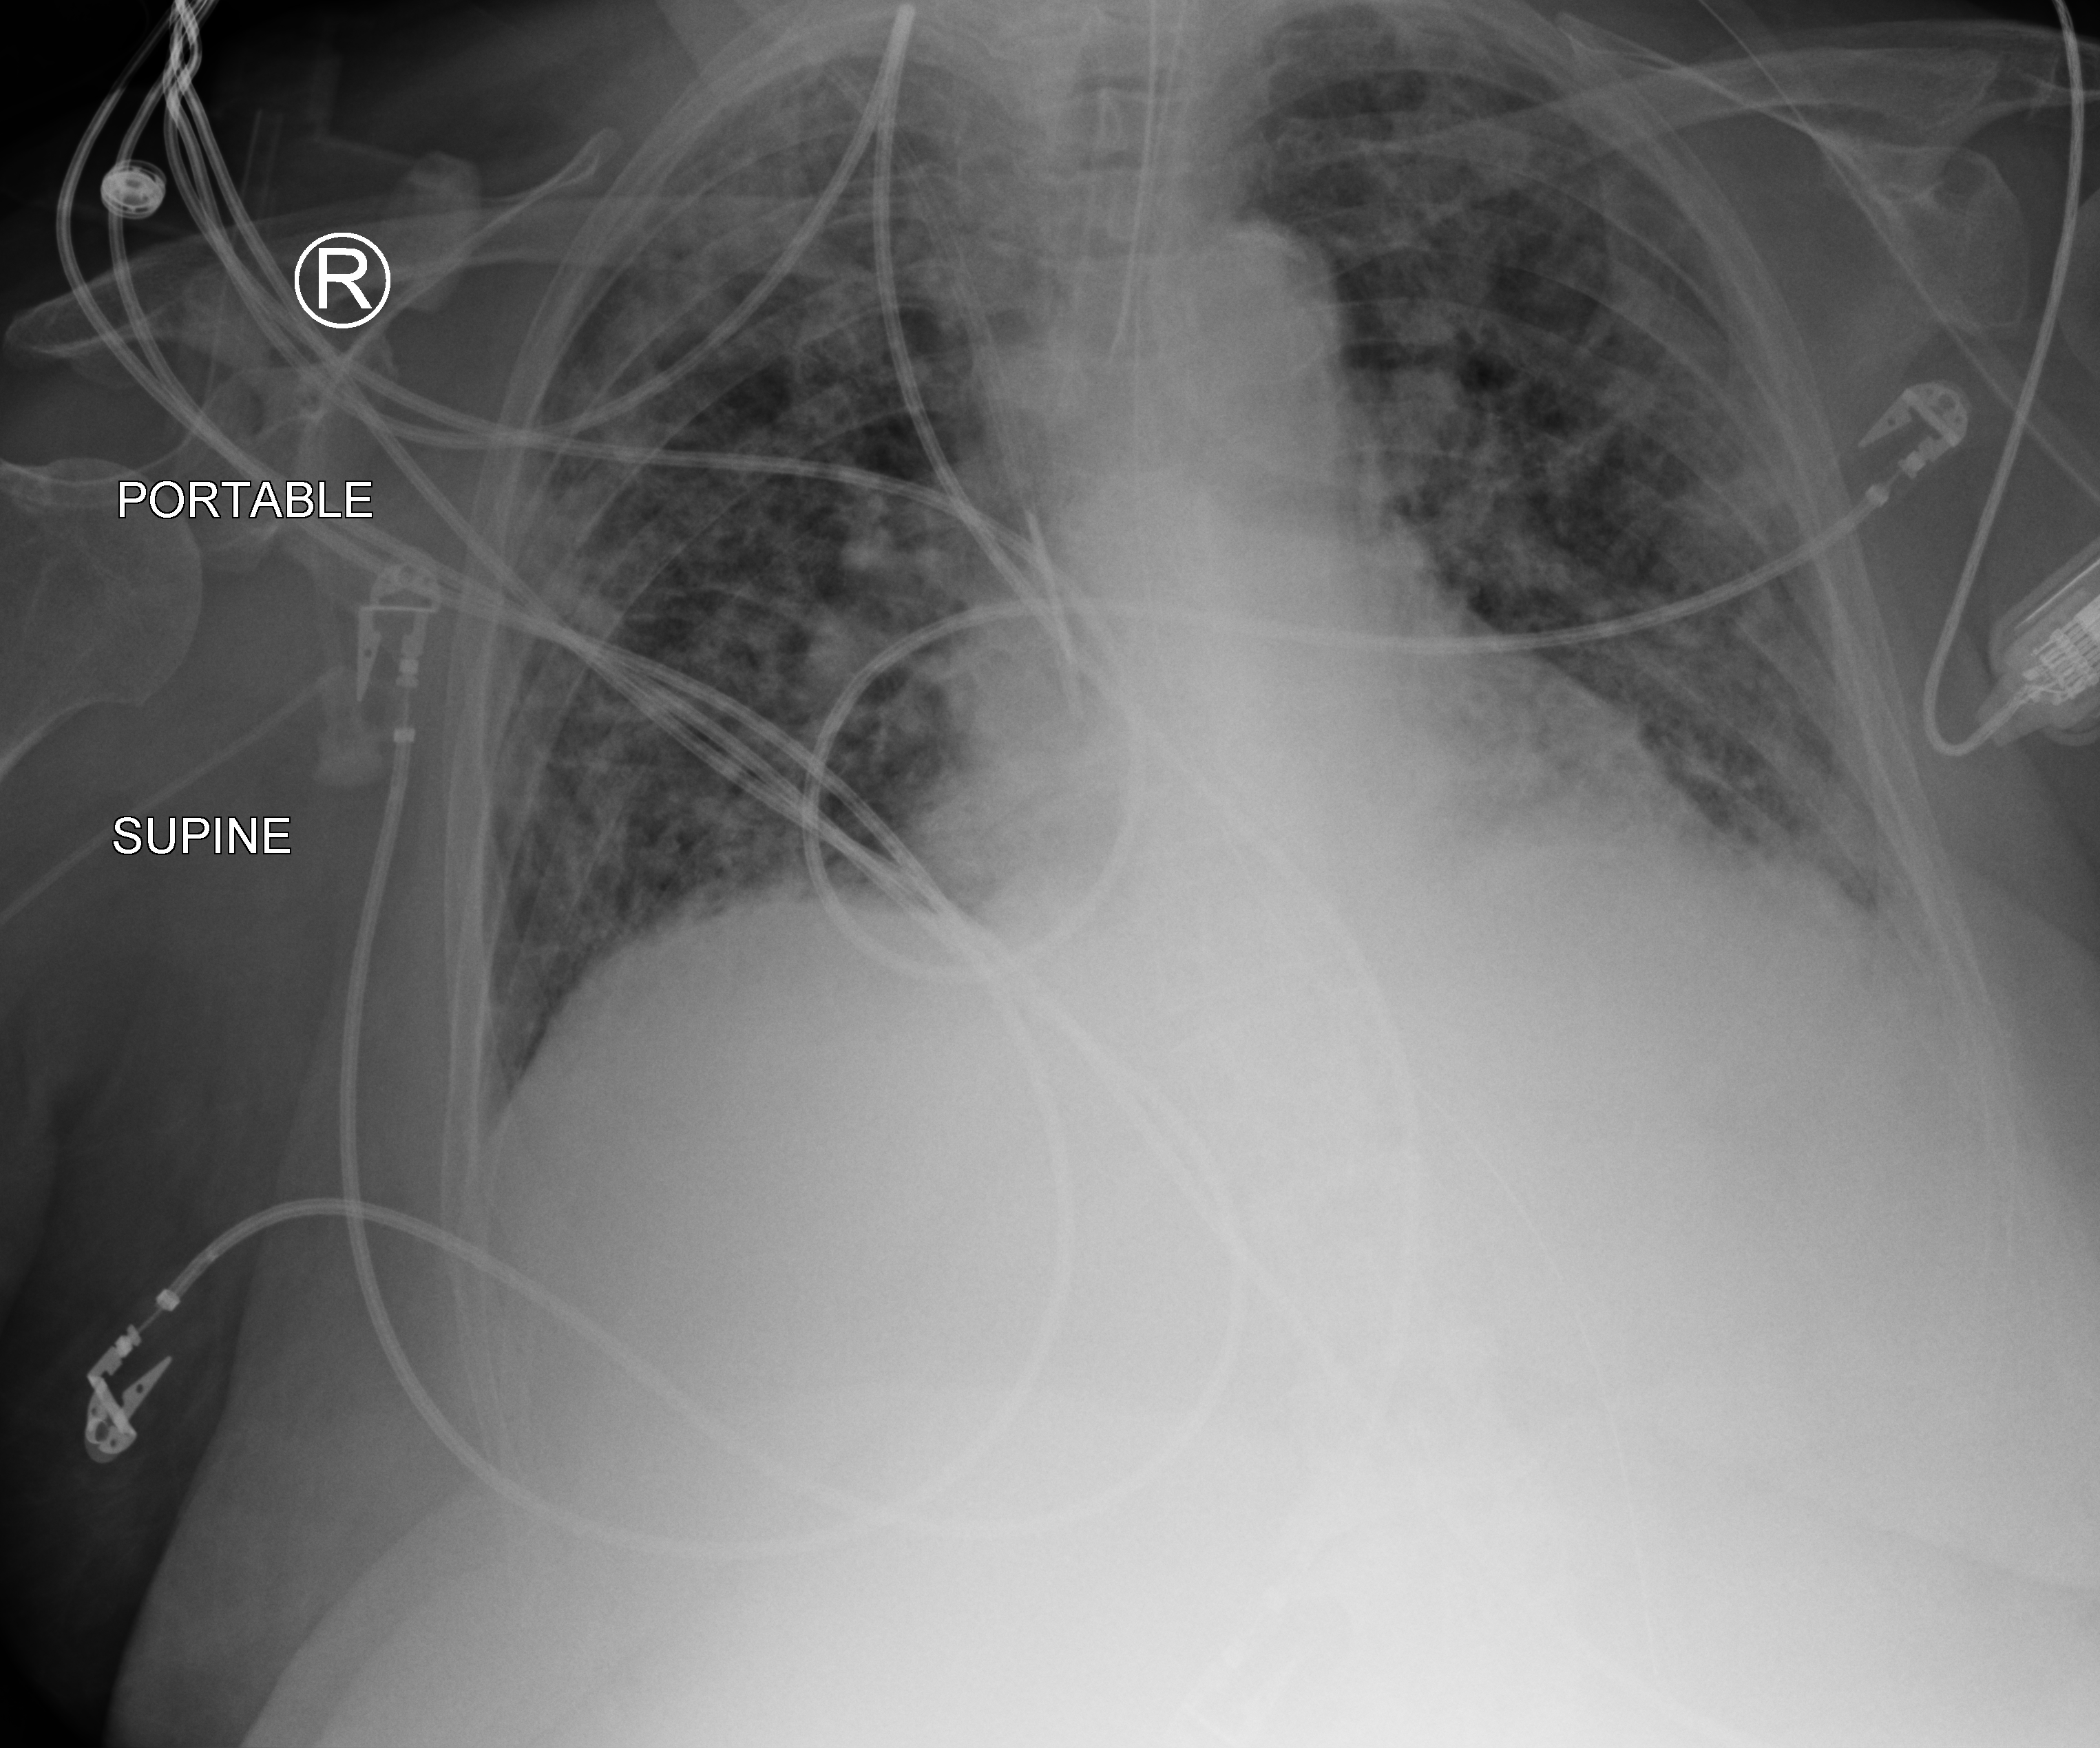
Portable chest radiograph, anteroposterior (AP) projection. Patient hospitalised with COVID-19; female, aged 75–90 years.
Admission-level facts for this patient (not findings on this image; timing relative to this image not recorded): mechanically ventilated during this hospital stay: yes; hypertension (admission record): yes; COPD (admission record): no.